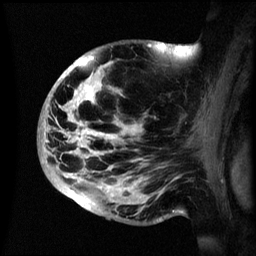
Breast MRI (dynamic contrast-enhanced), one sagittal slice. Slice 37 of 60 in the series (ordered by position). Dynamic contrast-enhanced series, image 2 of 3 at this slice position (ordered by acquisition). 1.5 T. TE 4.2 ms, TR 8.4 ms. 256 × 256 image matrix, field of view 230 × 230 mm. Patient: female, 48 years.
Structures marked on this image (semi-automatic segmentation, software-assisted and operator-edited):
- analysis volume of interest (the breast-tissue region the enhancement analysis was run in; not a lesion): bounding box [x1, y1, x2, y2] px = [39, 42, 195, 222]
- tumour enhancement mask (voxels above the 70 % enhancement threshold inside the analysis volume of interest): [44, 56, 136, 212]